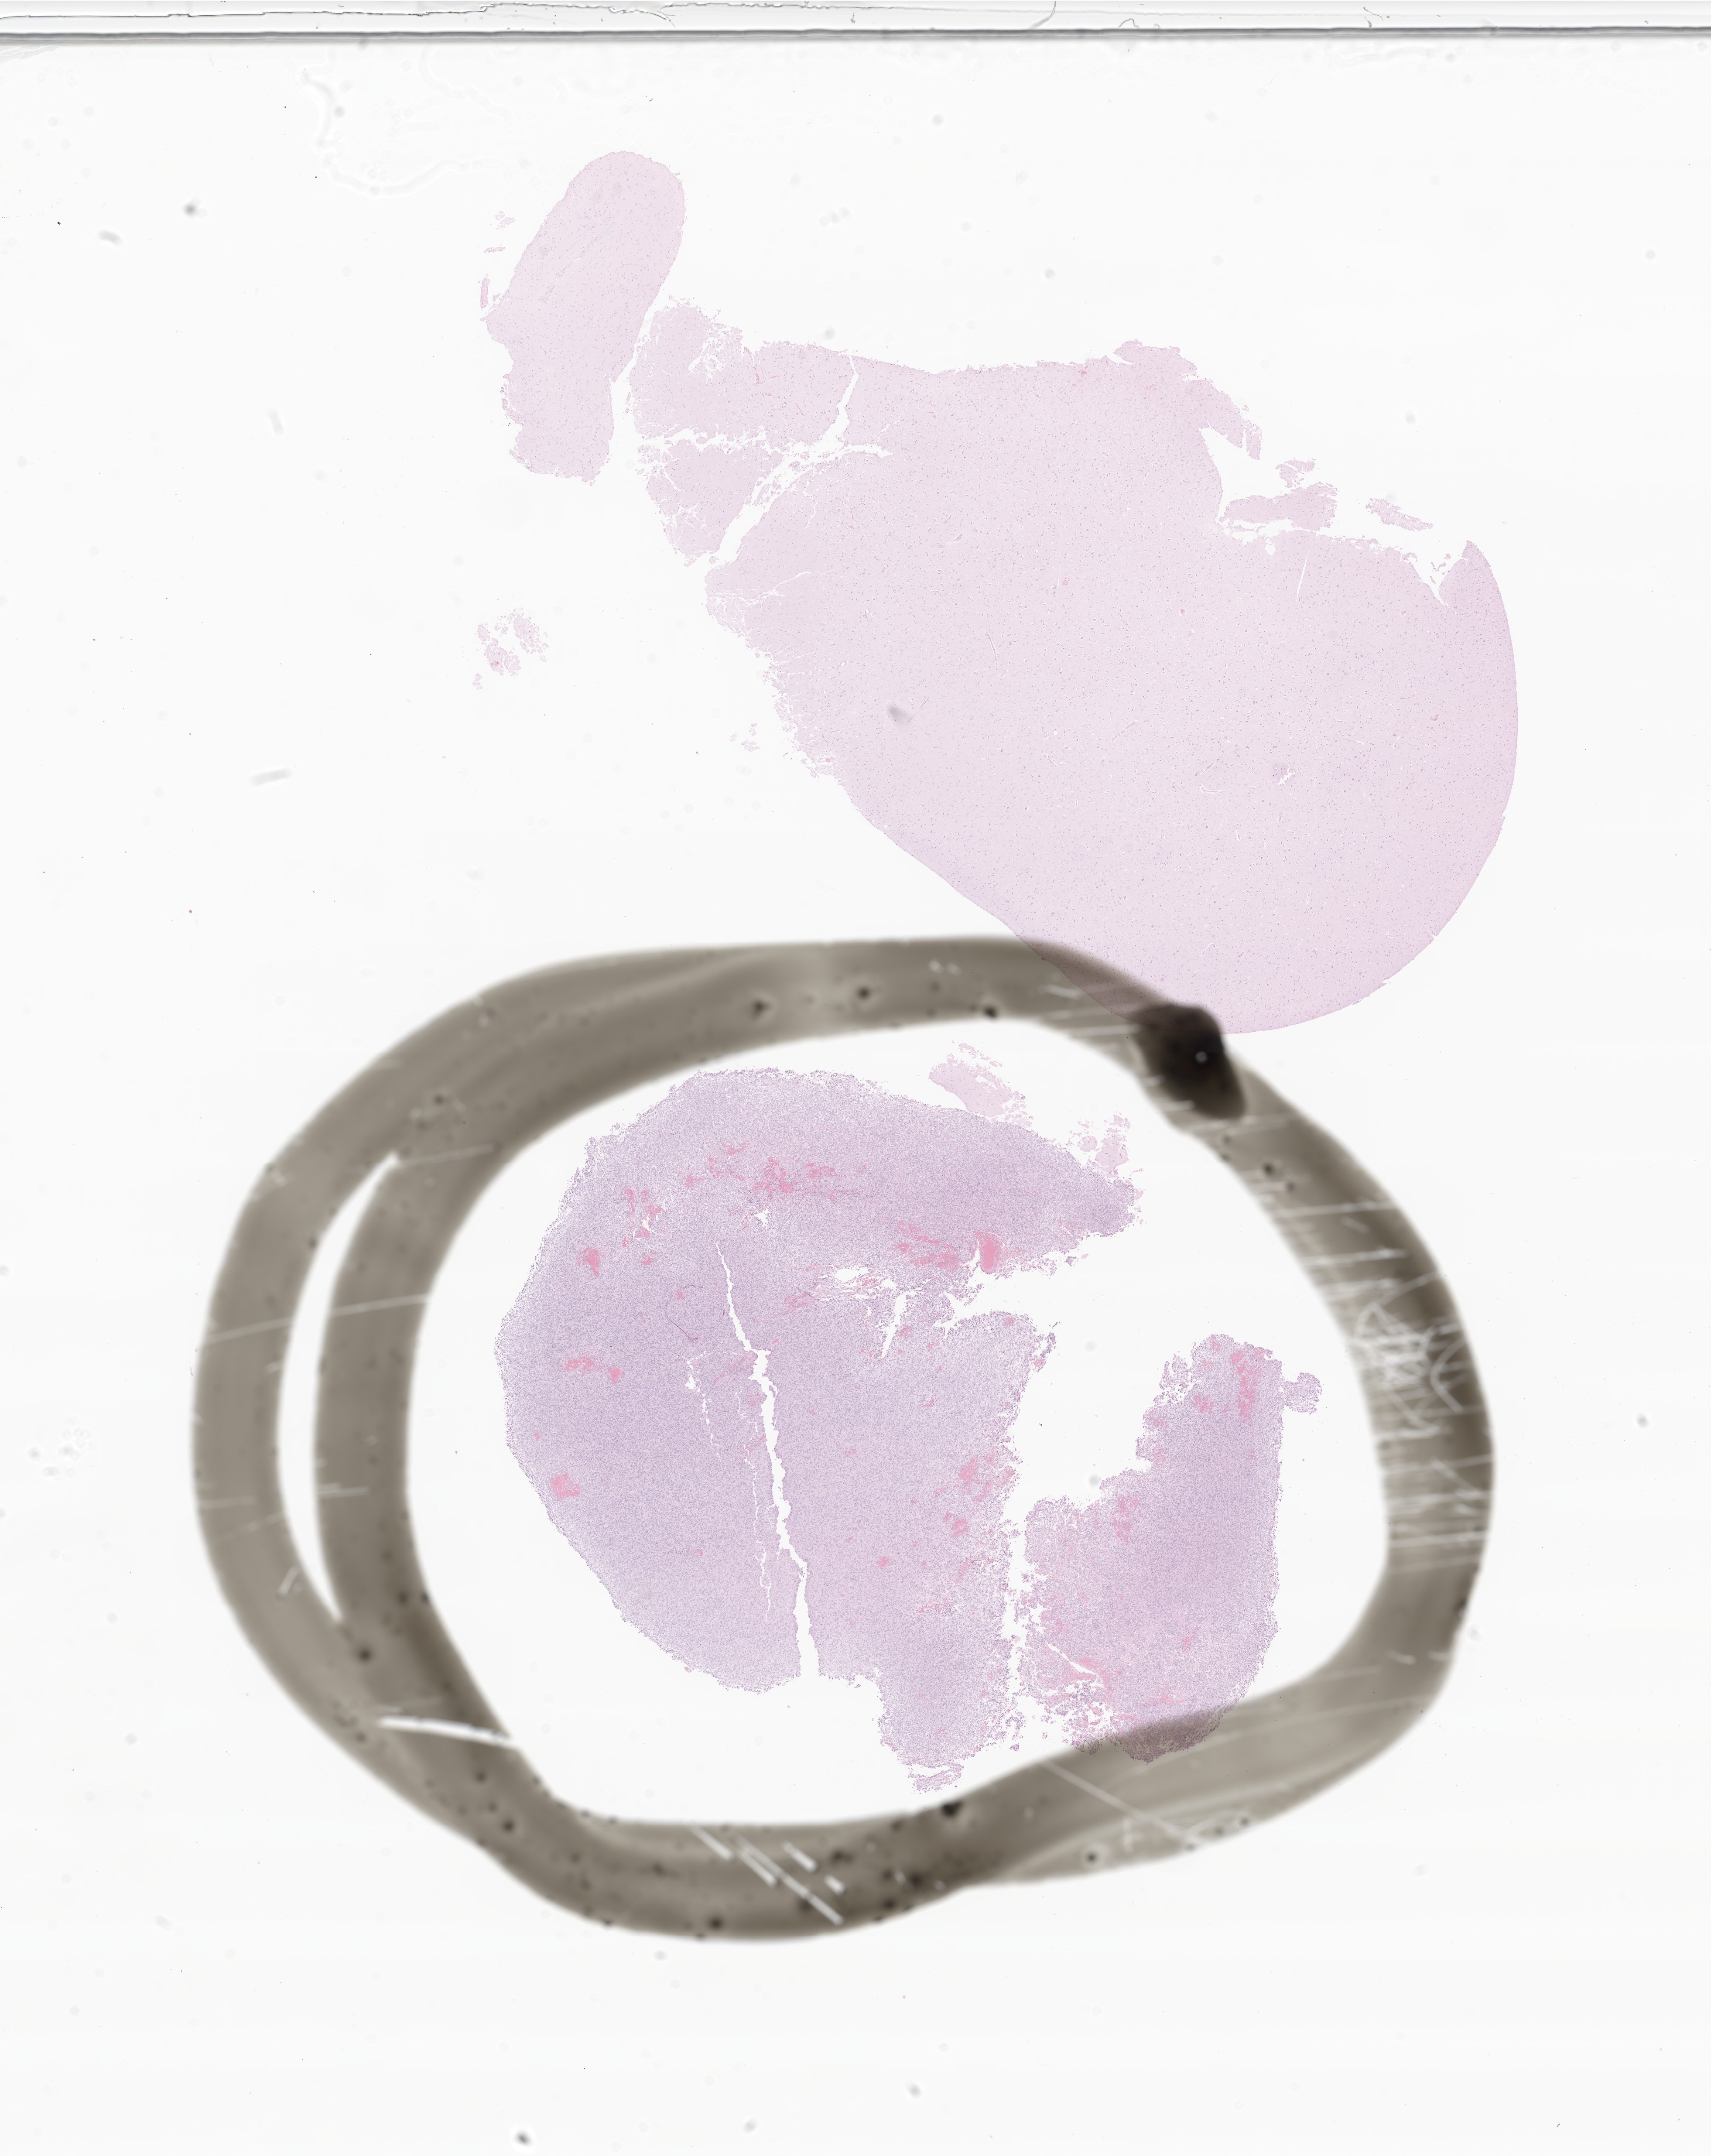
Haematoxylin and eosin whole-slide image of tumor tissue from the blood, low-resolution overview of the scanned area, about 16.5 x 20.8 mm. Male patient, age 397 months (33 years 1 month).
Specimen: FFPE section.